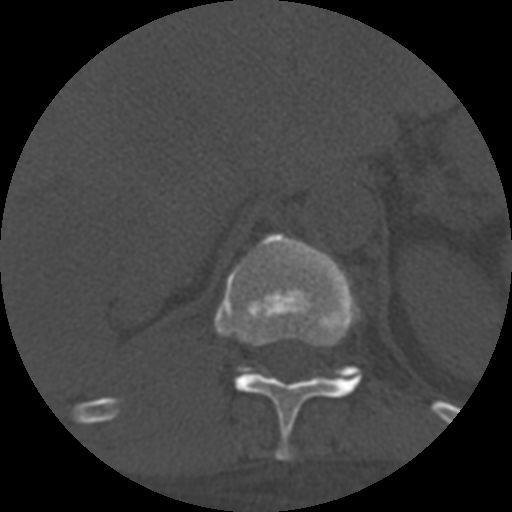
CT including the spine, one axial slice; position 330 of 708 along the scan axis; reconstruction kernel STANDARD; one of 3 acquisitions stored at this slice position; bone window (W 1800 / L 400 HU); 512 × 512 image matrix, field of view 160 × 160 mm. Patient age 55 years. From the clinical record (not read from this slice): primary cancer: colon; vertebrae with lytic lesions (as recorded): T12, L1, L5.
Outlined on this slice (semi-automatically segmented with operator editing):
- T11 vertebra: bounding box (x1, y1, x2, y2) in pixels: (216, 233, 361, 461)
- T12 vertebra: (321, 366, 362, 380)